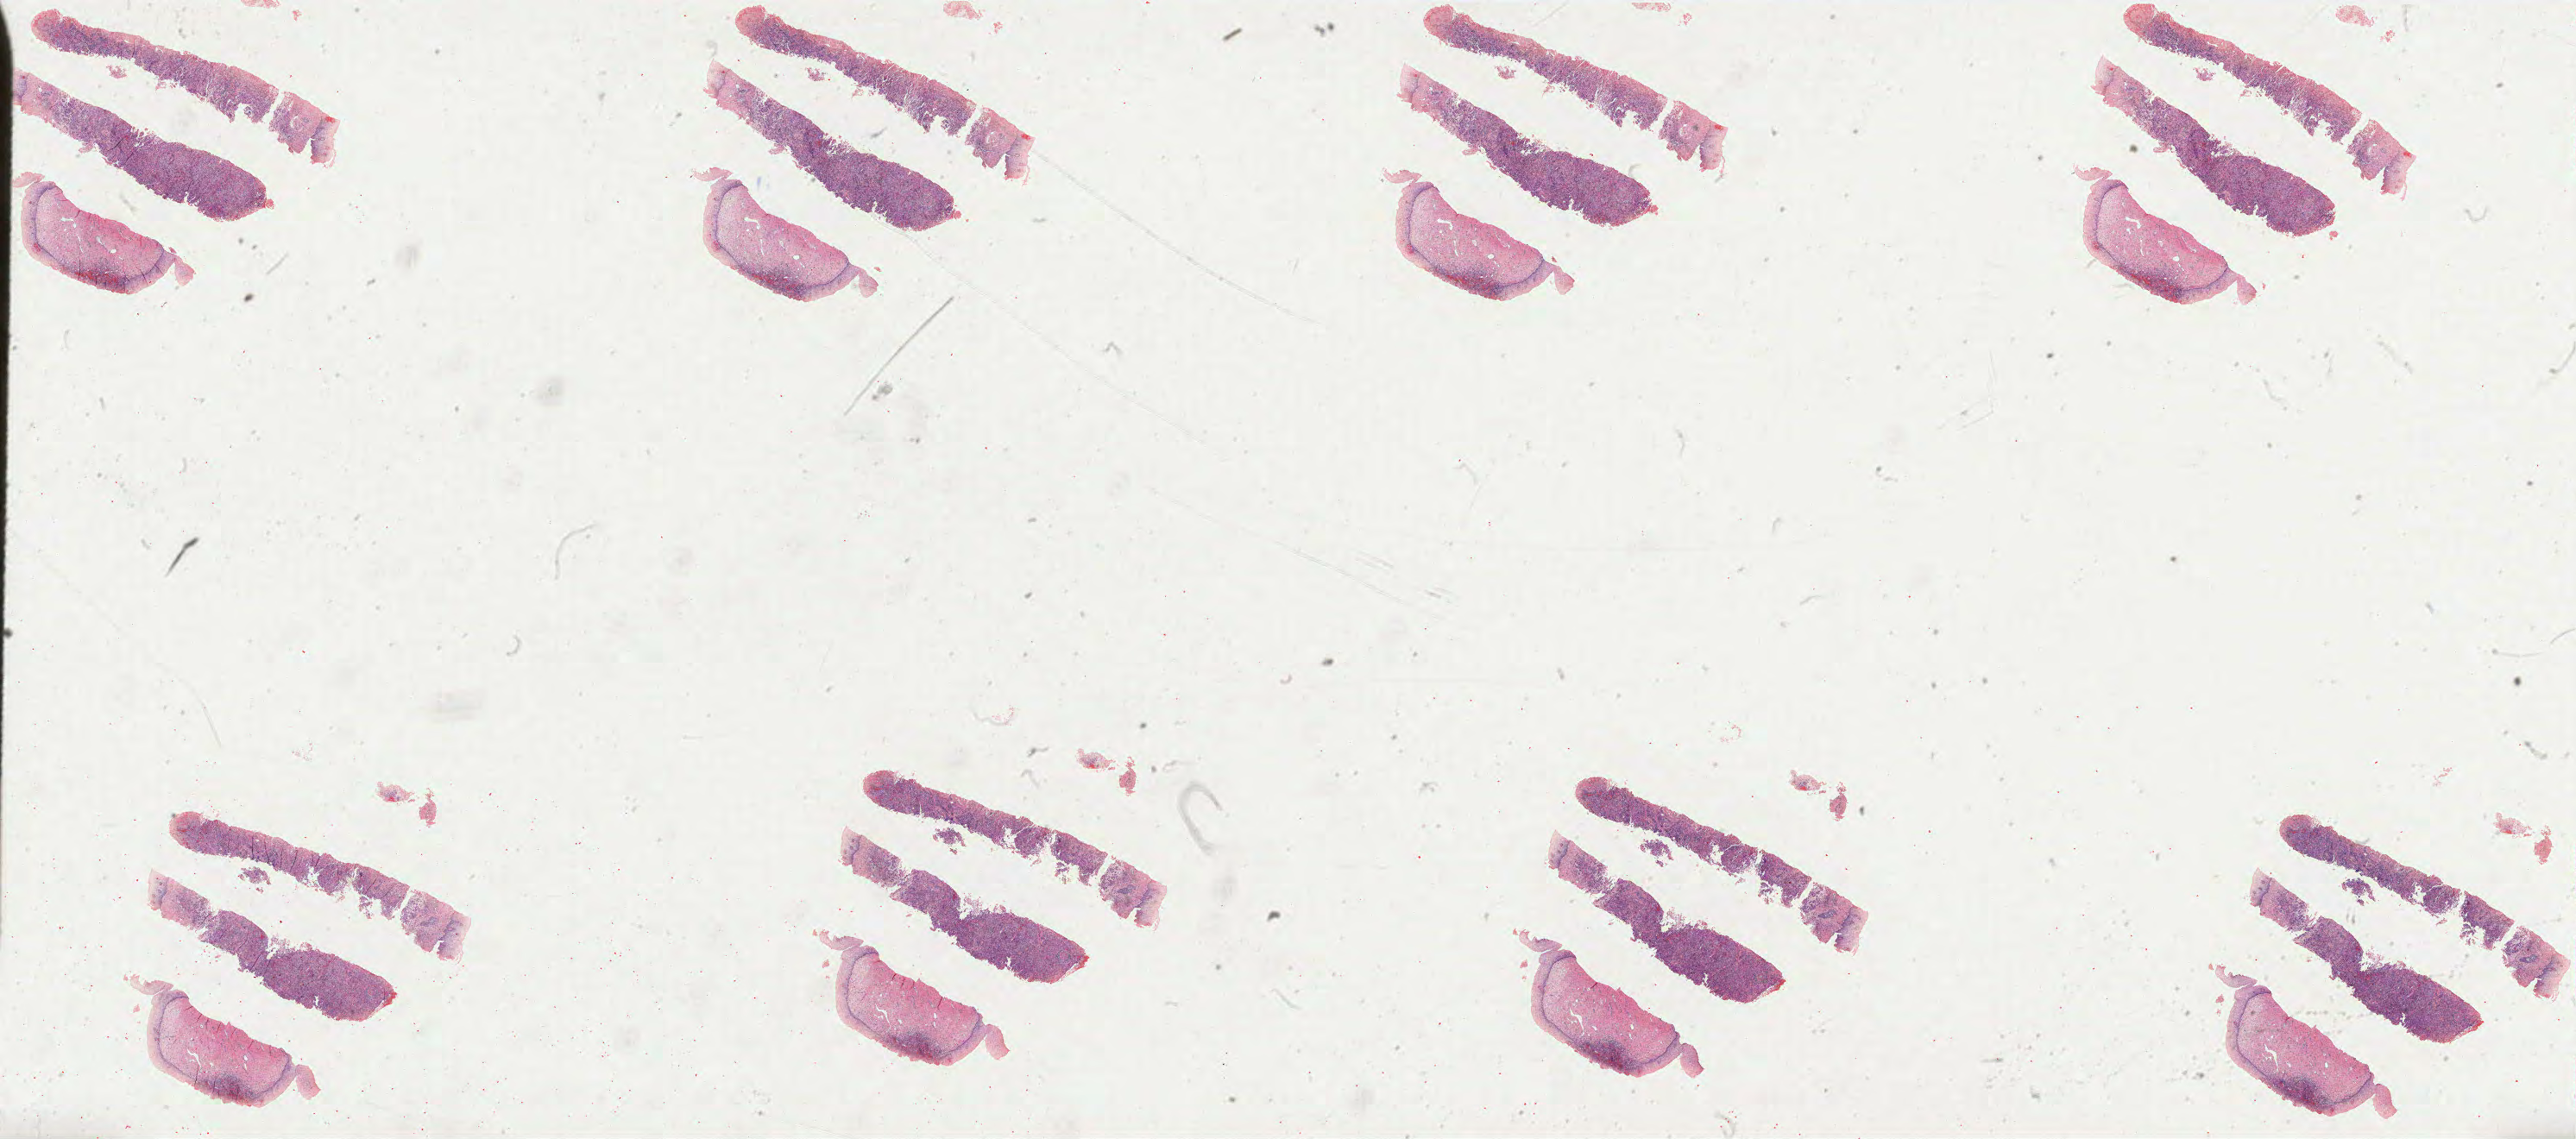
Whole-slide histology image, H&E — shown as a low-resolution overview of the whole scanned area (about 47.8 x 21.1 mm, slide scanned at 40x). FFPE section. Primary tumour sample from the cervix. Female, age 36 years at initial diagnosis. Histologic grade: G3 (poorly differentiated).
Histologic diagnosis: Squamous cell carcinoma, NOS (cervix uteri). FIGO stage: IB1.